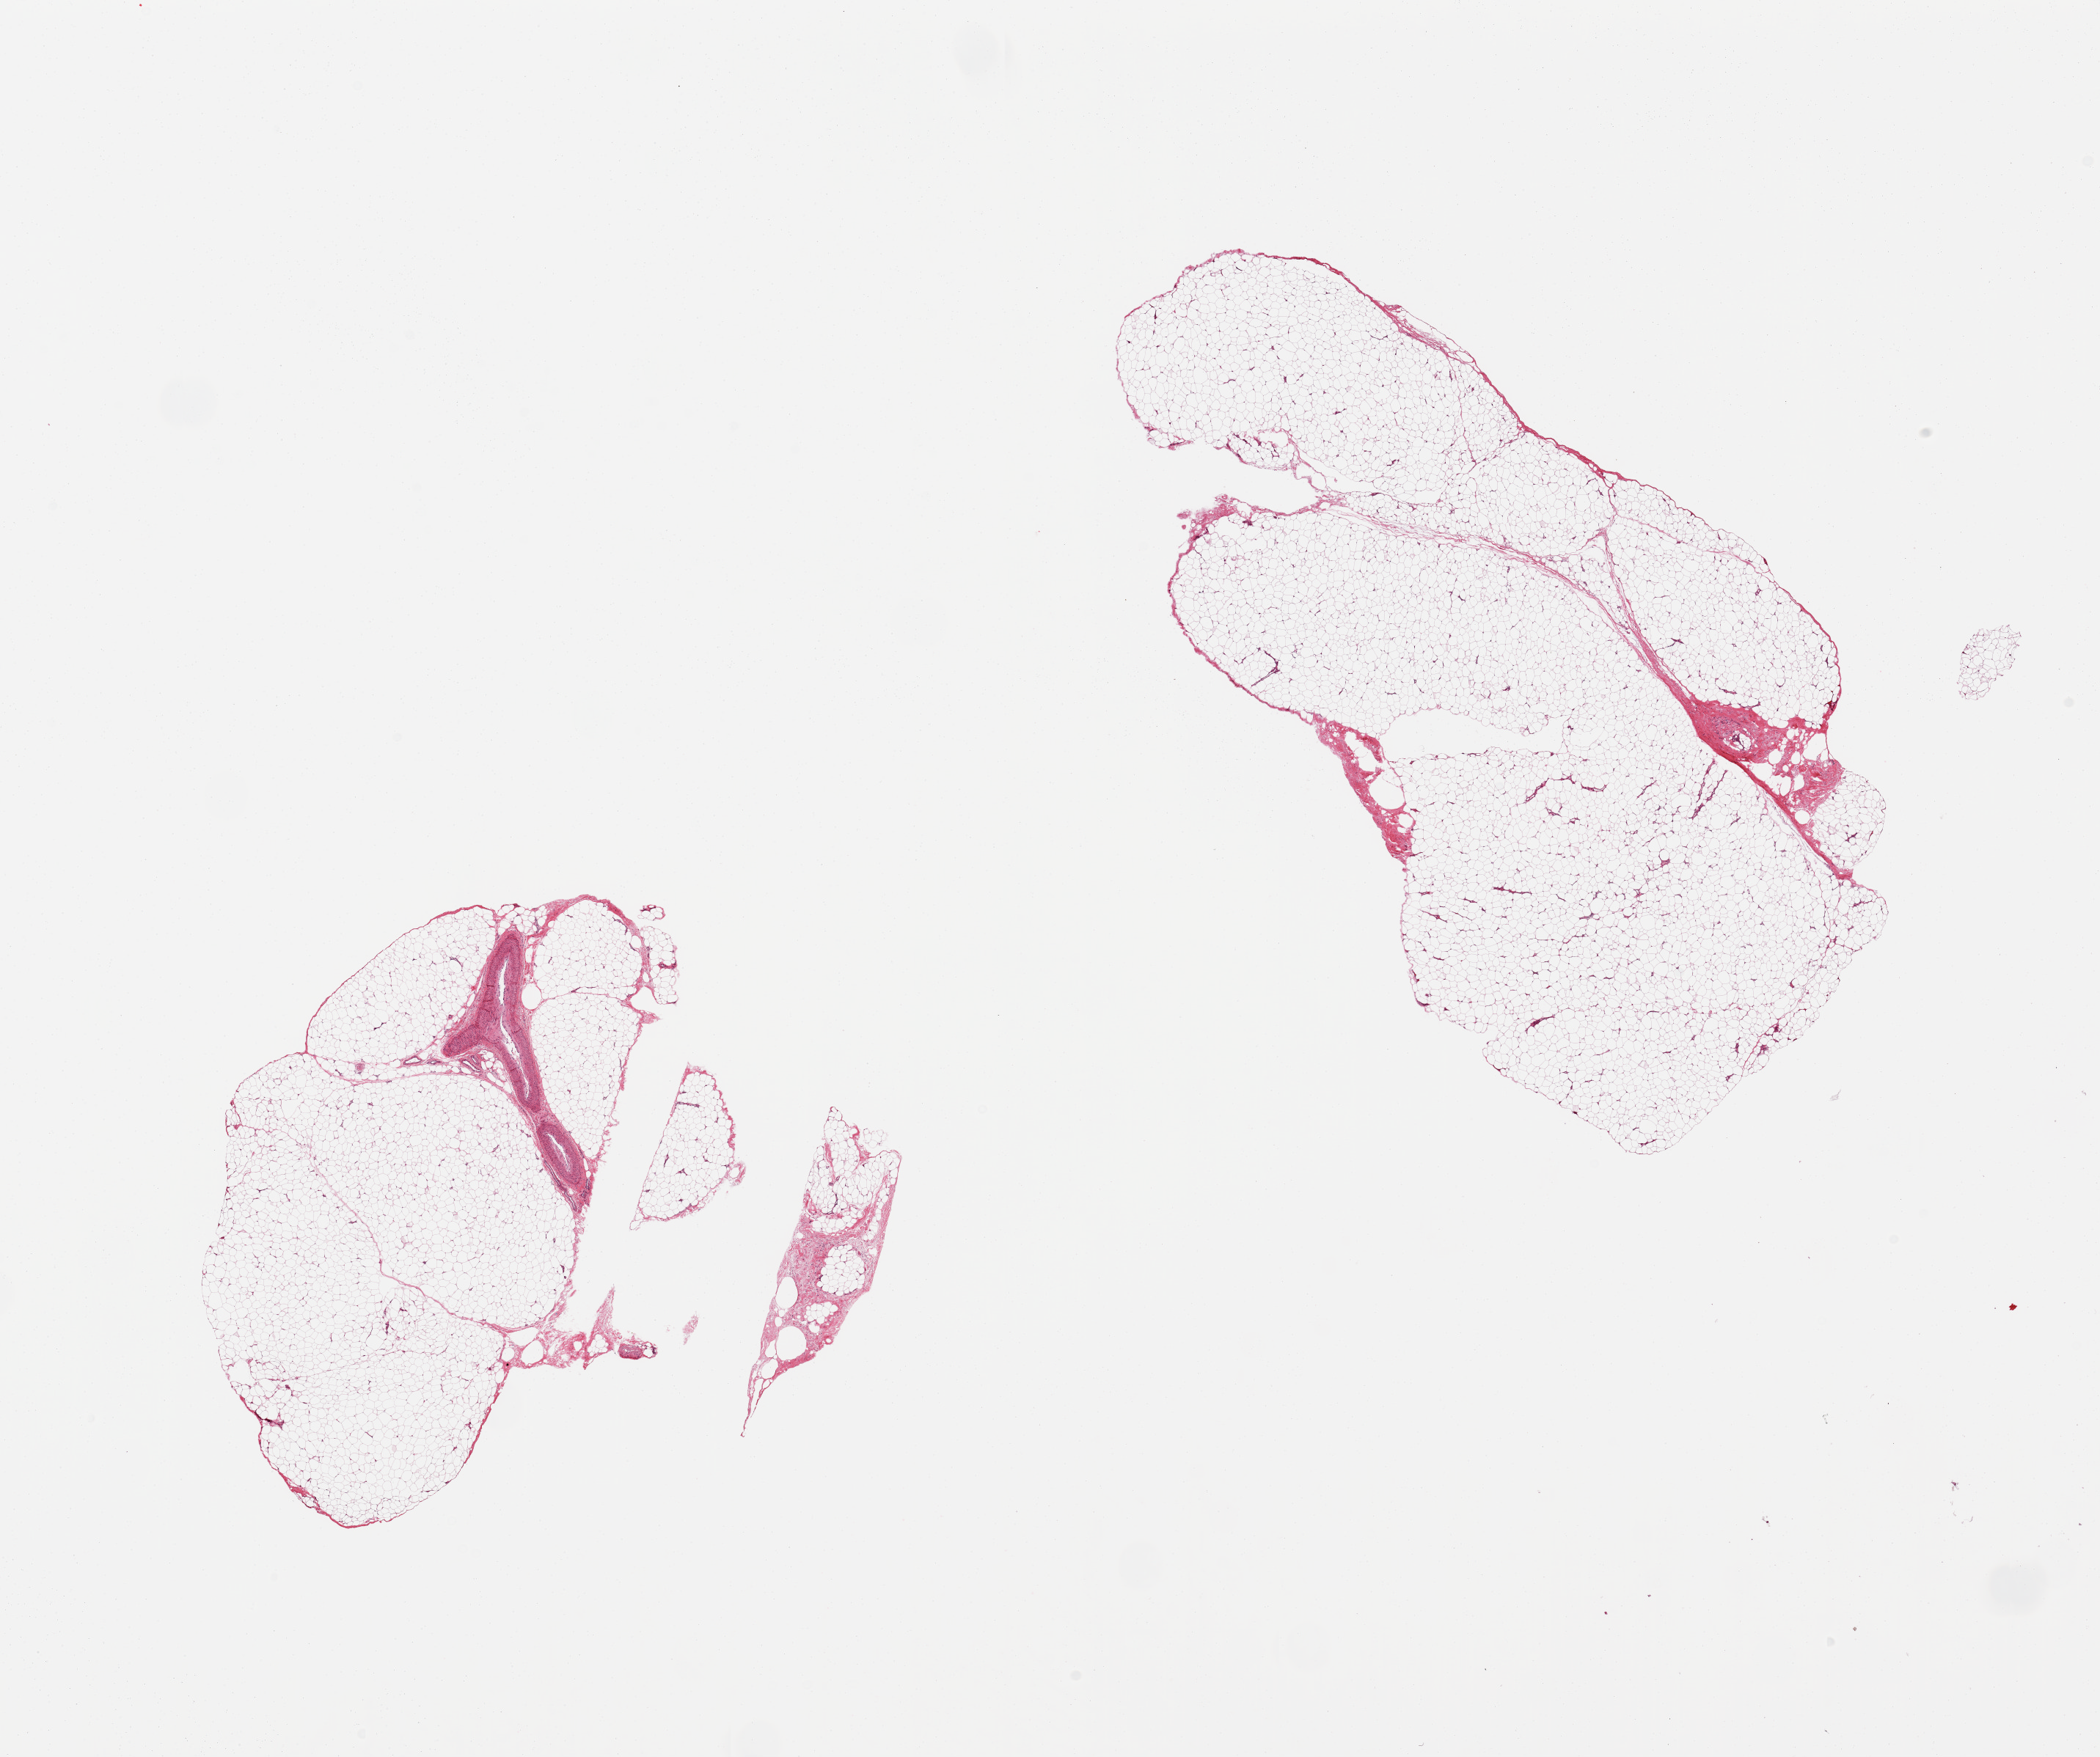
Digitized H&E-stained section, brightfield — a low-resolution overview of the entire scanned area, about 22.6 x 18.9 mm. PAXgene-fixed, paraffin-embedded tissue. Target tissue: adipose tissue. Donor tissue sample. Female donor.
Review note (as recorded): 2 pieces, ~5-10% fibro-fascial/vascular tissue.